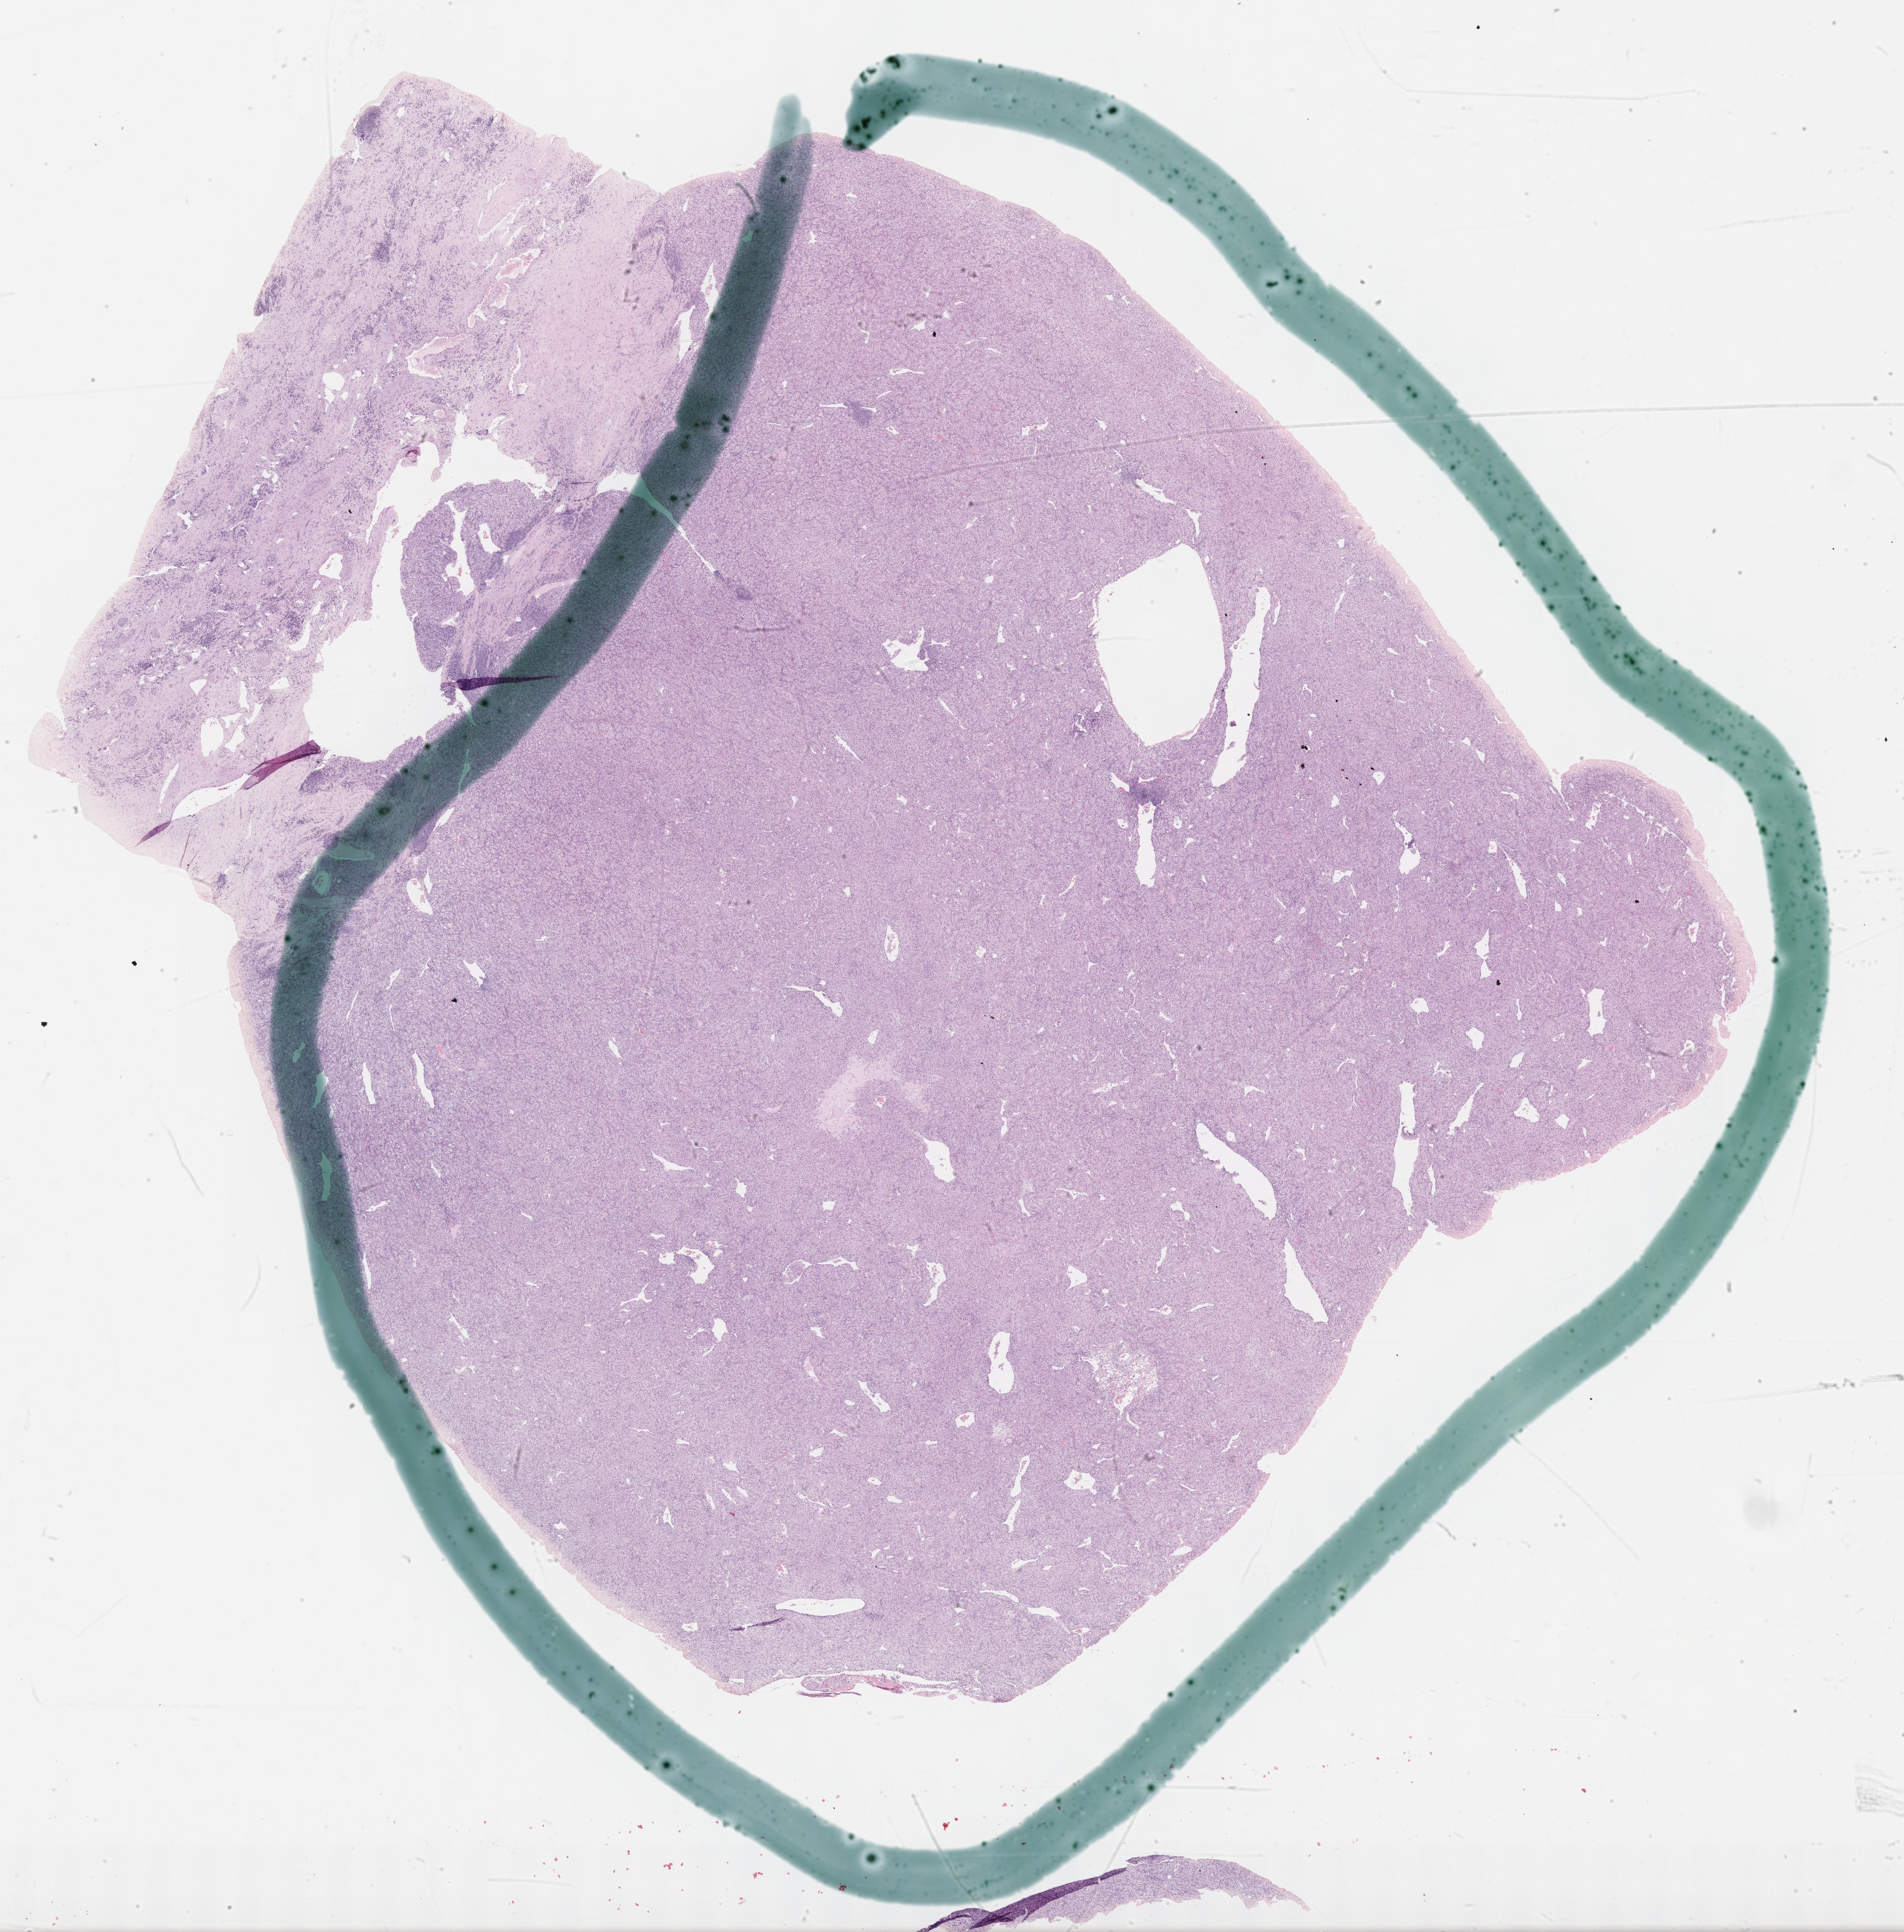
Digitized Hematoxylin and eosin (H&E) stained tissue section (whole slide) — whole scanned area (about 21.1 x 21.4 mm) shown as a low-resolution overview; FFPE section; sample: primary tumour, kidney. Male patient; age at initial diagnosis 49 years. Histologic grade: G2 (moderately differentiated).
* lymph nodes positive (case pathology): 3 of 10 examined
* AJCC pathologic stage: III
* histologic diagnosis: Clear cell adenocarcinoma, NOS
* laterality: right